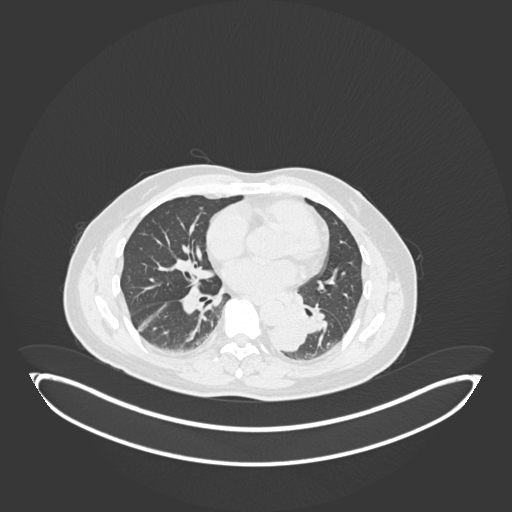
Chest CT, one axial slice; slice 86 of 258 in the series (ordered by position); reconstruction kernel B30f; 120 kVp; lung window (W 1500 / L -600 HU); 512 × 512 image matrix, field of view 500 × 500 mm. Patient: male, 54 years. Case-level facts recorded for this patient, not image findings: clinical TNM (as recorded): T3 N0 M0.
Outlined on this slice (bounding box drawn by a radiologist):
- lung tumour (recorded histology: squamous cell carcinoma): bounding box [x1, y1, x2, y2] px = [270, 303, 313, 356]